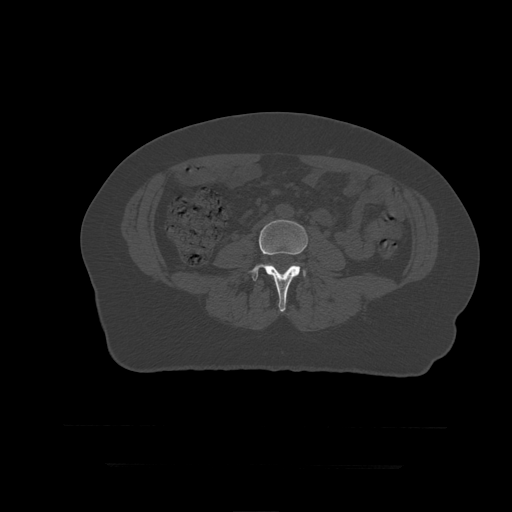
CT including the spine, one axial slice; slice 94 of 399 in the series (ordered by position); reconstruction kernel STANDARD; 120 kVp; bone window (W 1800 / L 400 HU); 512 × 512 image matrix, field of view 450 × 450 mm. Patient age 41 years. Case-level facts recorded for this patient, not image findings: primary cancer: breast.
Outlined on this slice (semi-automatically segmented with operator editing):
- L4 vertebra: box from (x=249, y=220) to (x=308, y=312) px
- L5 vertebra: (x=303, y=270)–(x=306, y=277)